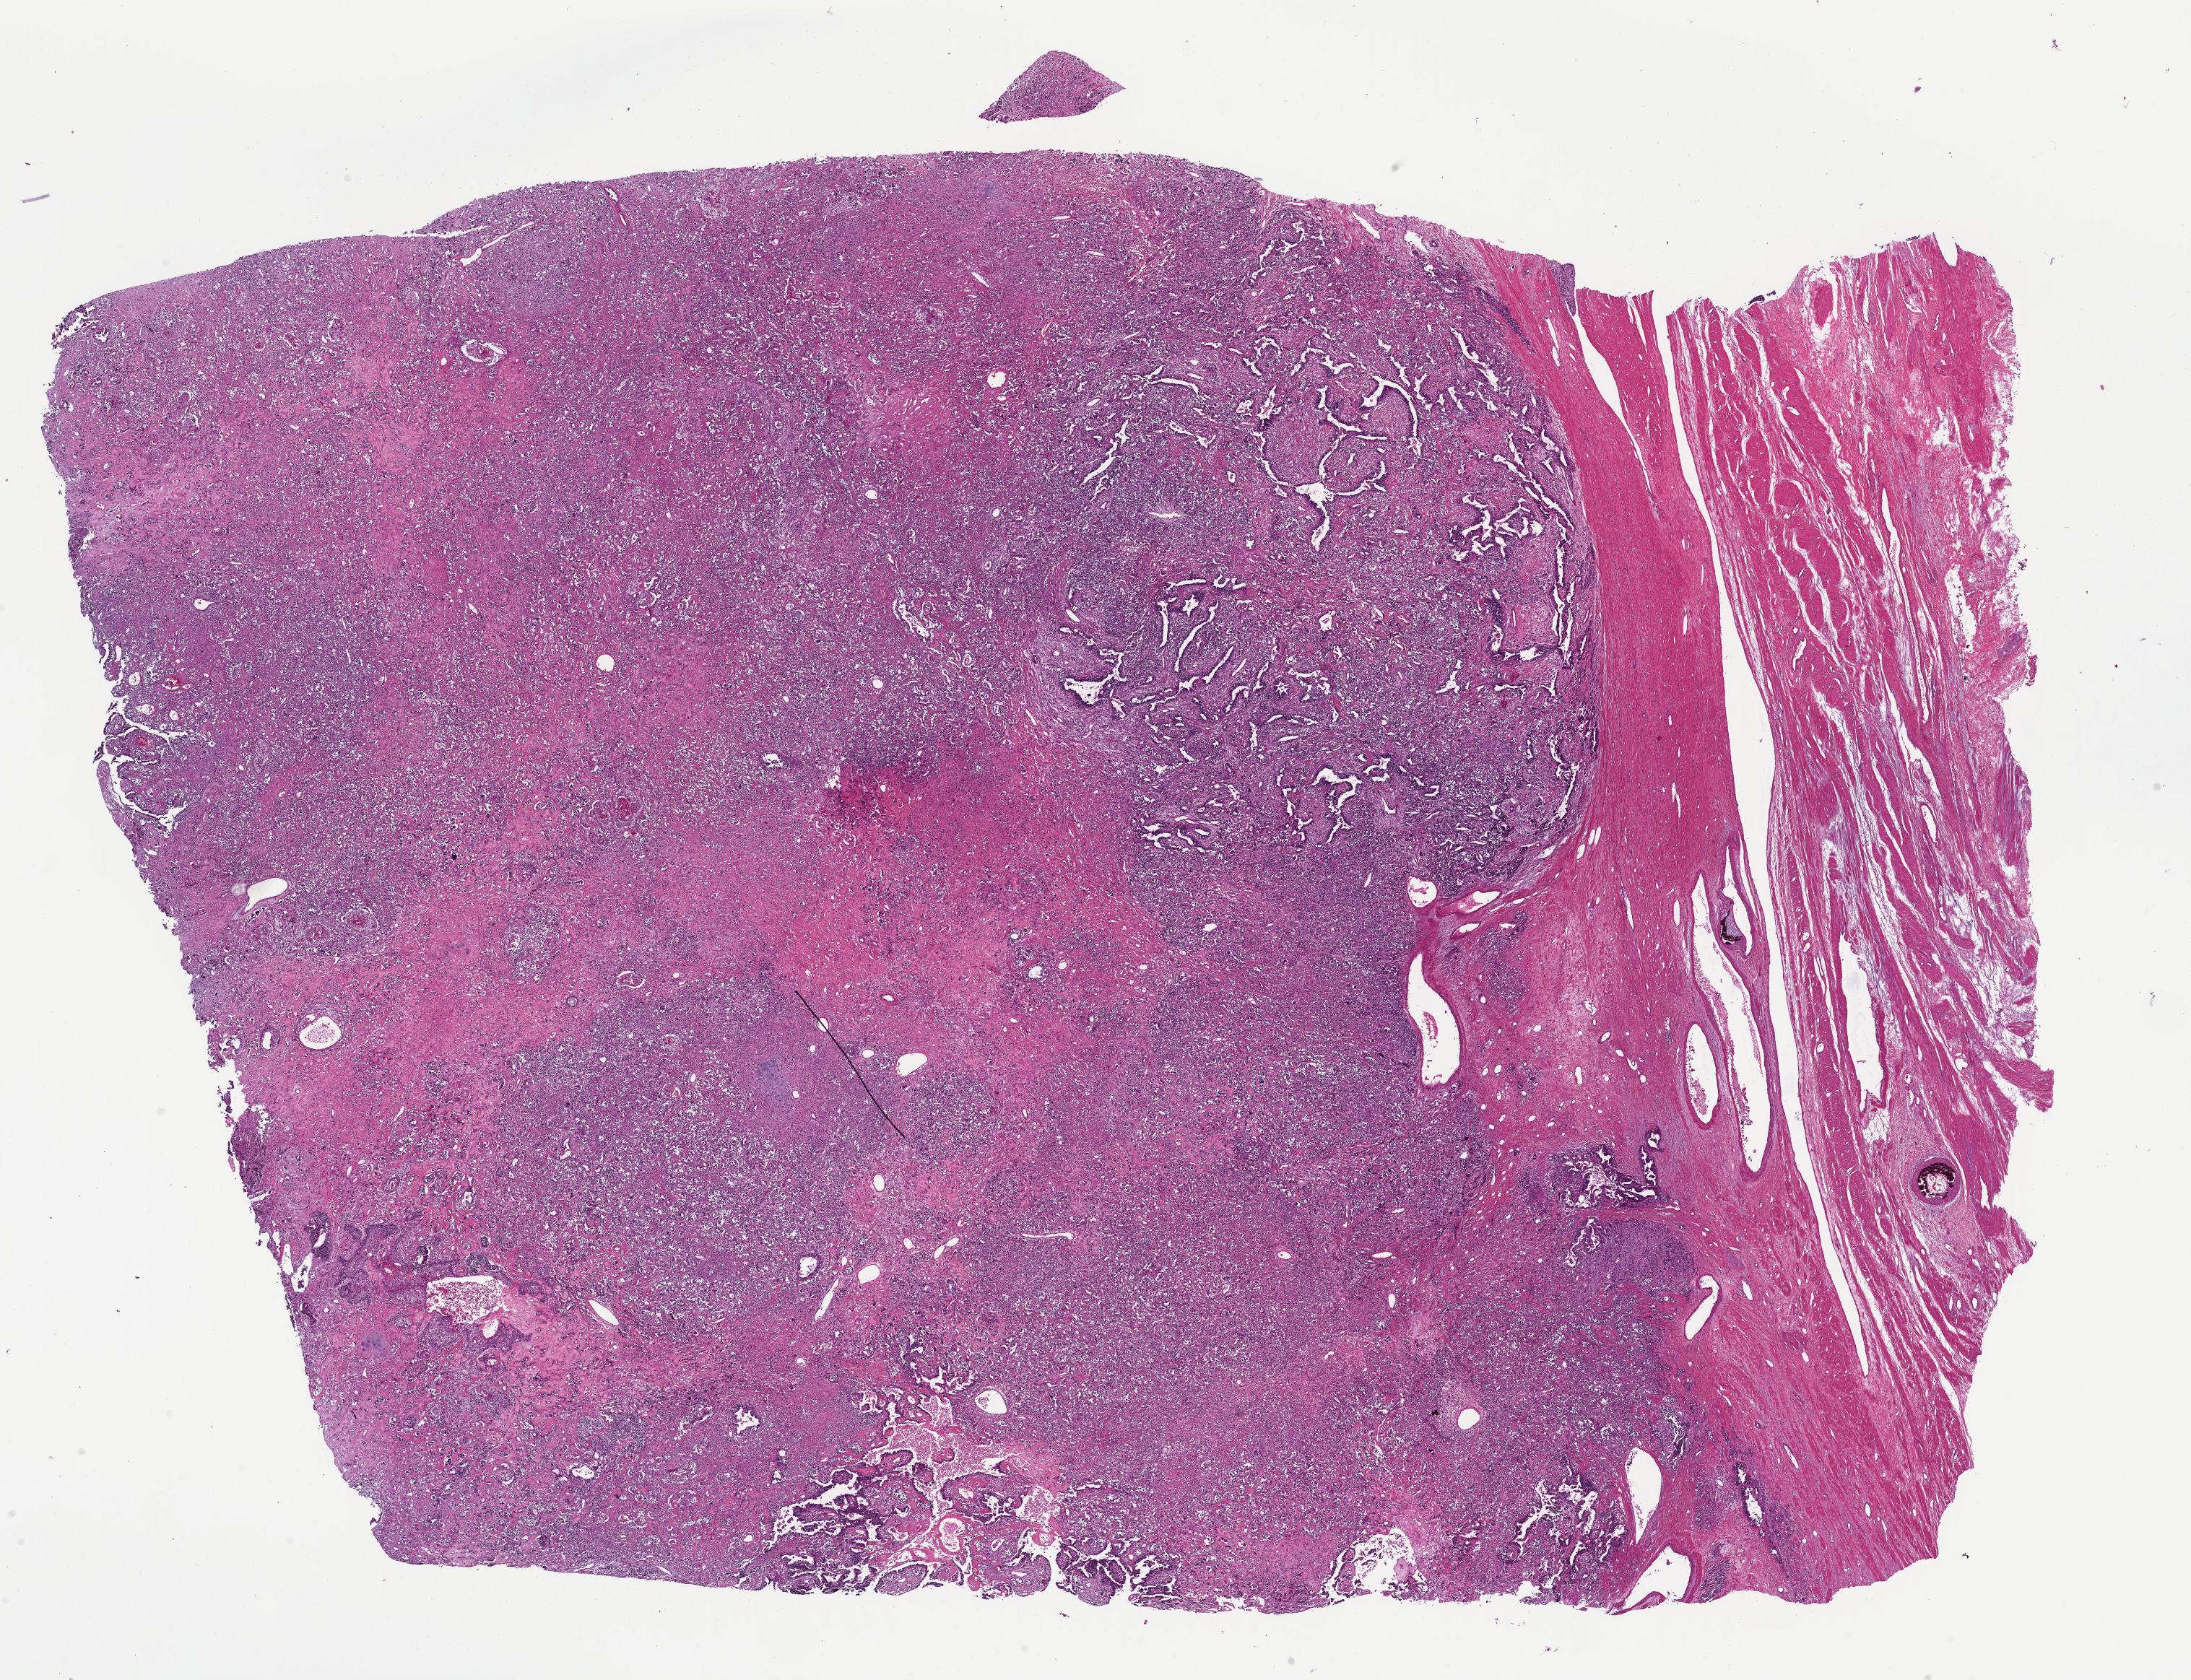
Whole-slide histology image, H&E-stained — shown as a low-resolution overview of the whole scanned area (about 23.9 x 18.4 mm, from a 40x scan). Formalin-fixed paraffin-embedded (FFPE) diagnostic section. Sample: primary tumour, uterus. Female patient; age at initial diagnosis 80 years.
FIGO stage: IIIB. Diagnosis: Carcinosarcoma, NOS.